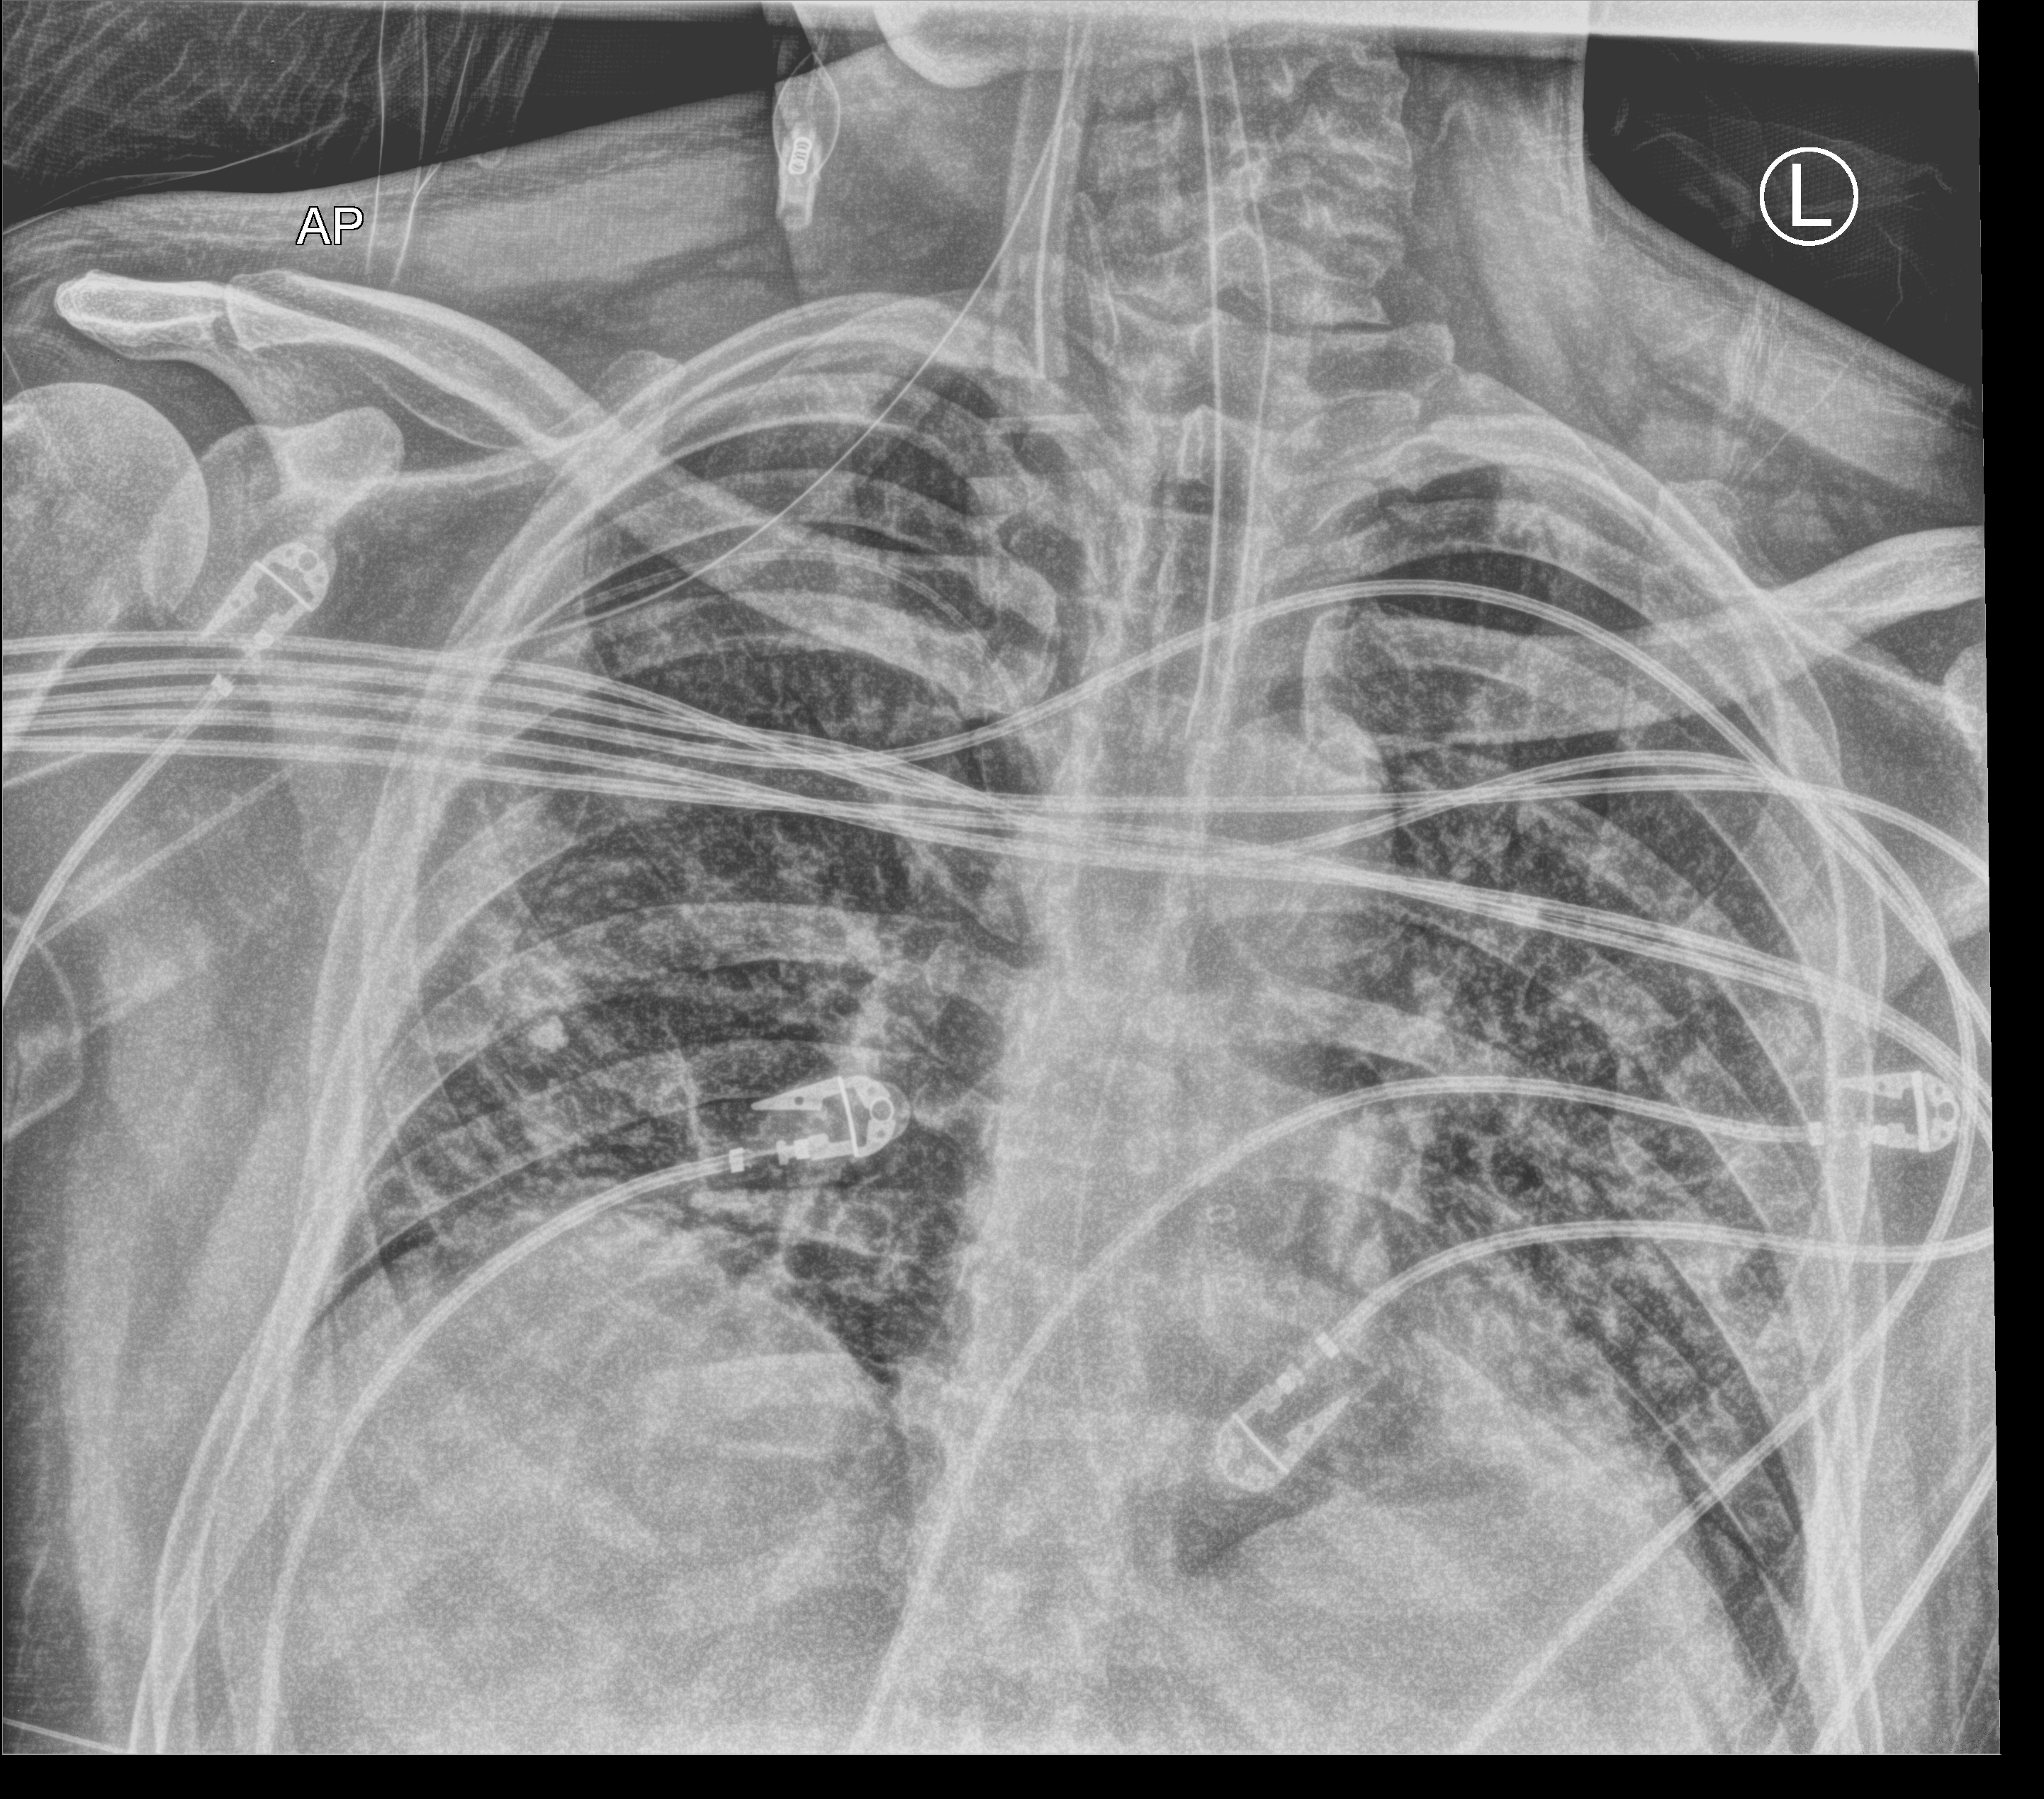
Bedside chest radiograph (computed radiography); anteroposterior (AP) projection. Patient hospitalised with COVID-19; male, aged 18–59 years.
Hospital-stay facts (about this admission, not read from this image; timing relative to this image not recorded): smoking status (admission record): never; other chronic lung disease (admission record): no; mechanically ventilated during this hospital stay: yes.